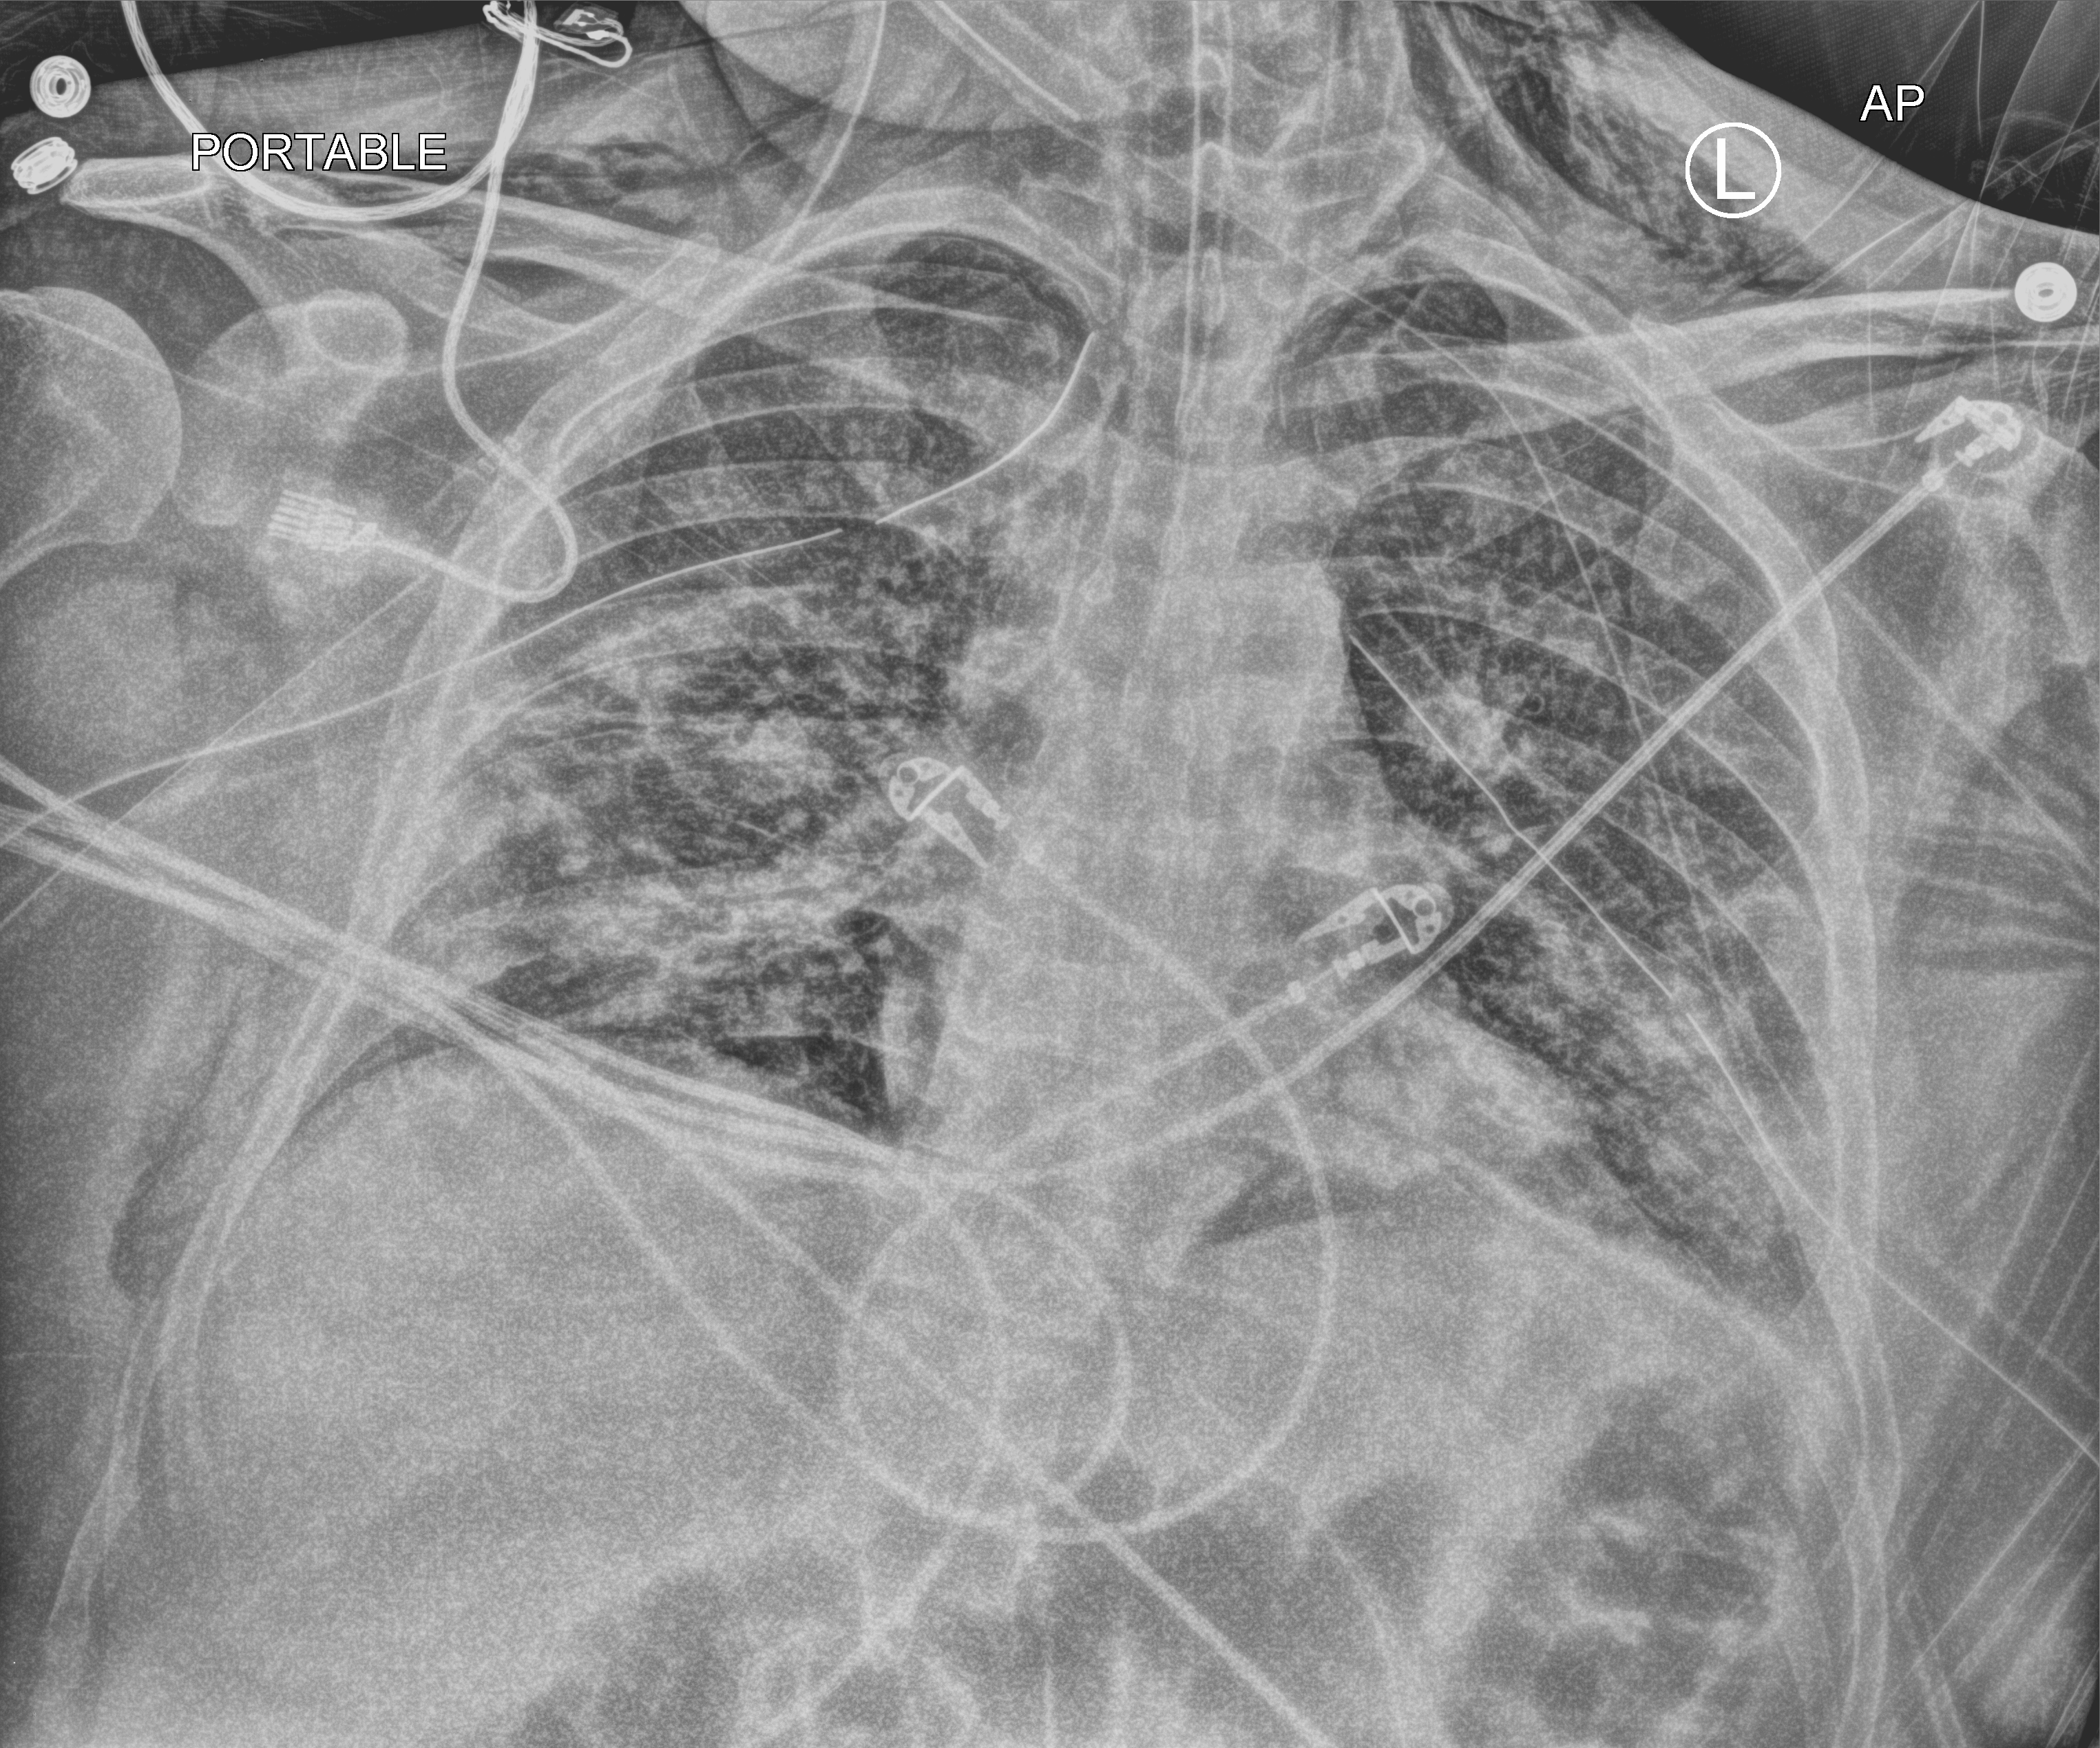
Bedside chest radiograph (computed radiography); anteroposterior (AP) projection. Patient hospitalised with COVID-19; male, aged 18–59 years.
From the hospital-stay record, not from the radiograph (when in the stay this image was taken is not recorded): chronic kidney disease (admission record): no; admitted to intensive care during this hospital stay: yes; diabetes (admission record): yes.